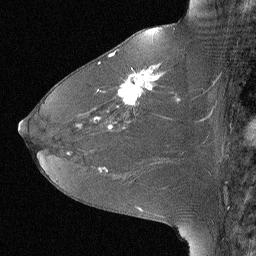
Breast MRI (dynamic contrast-enhanced), one sagittal slice. Slice 35 of 64 in the series (ordered by position). Dynamic contrast-enhanced study with each time point stored as its own series, time point 2 of 3 at this slice position (early post-contrast, ordered by acquisition time). 1.5 T. TE 4 ms, TR 30 ms. 256 × 256 image matrix, field of view 180 × 180 mm. Patient: female, 46 years. From the clinical record (not read from this slice): setting: breast cancer imaged before/during neoadjuvant chemotherapy; receptor status: HR-positive, HER2-negative.
Annotated regions visible in this slice (semi-automatic segmentation, software-assisted and operator-edited):
- analysis volume of interest (the breast-tissue region the enhancement analysis was run in; not a lesion): bounding box <106,43,184,119> (left, top, right, bottom; pixels)
- tumour enhancement mask (voxels above the 90 % enhancement threshold inside the analysis volume of interest): <109,52,179,105>